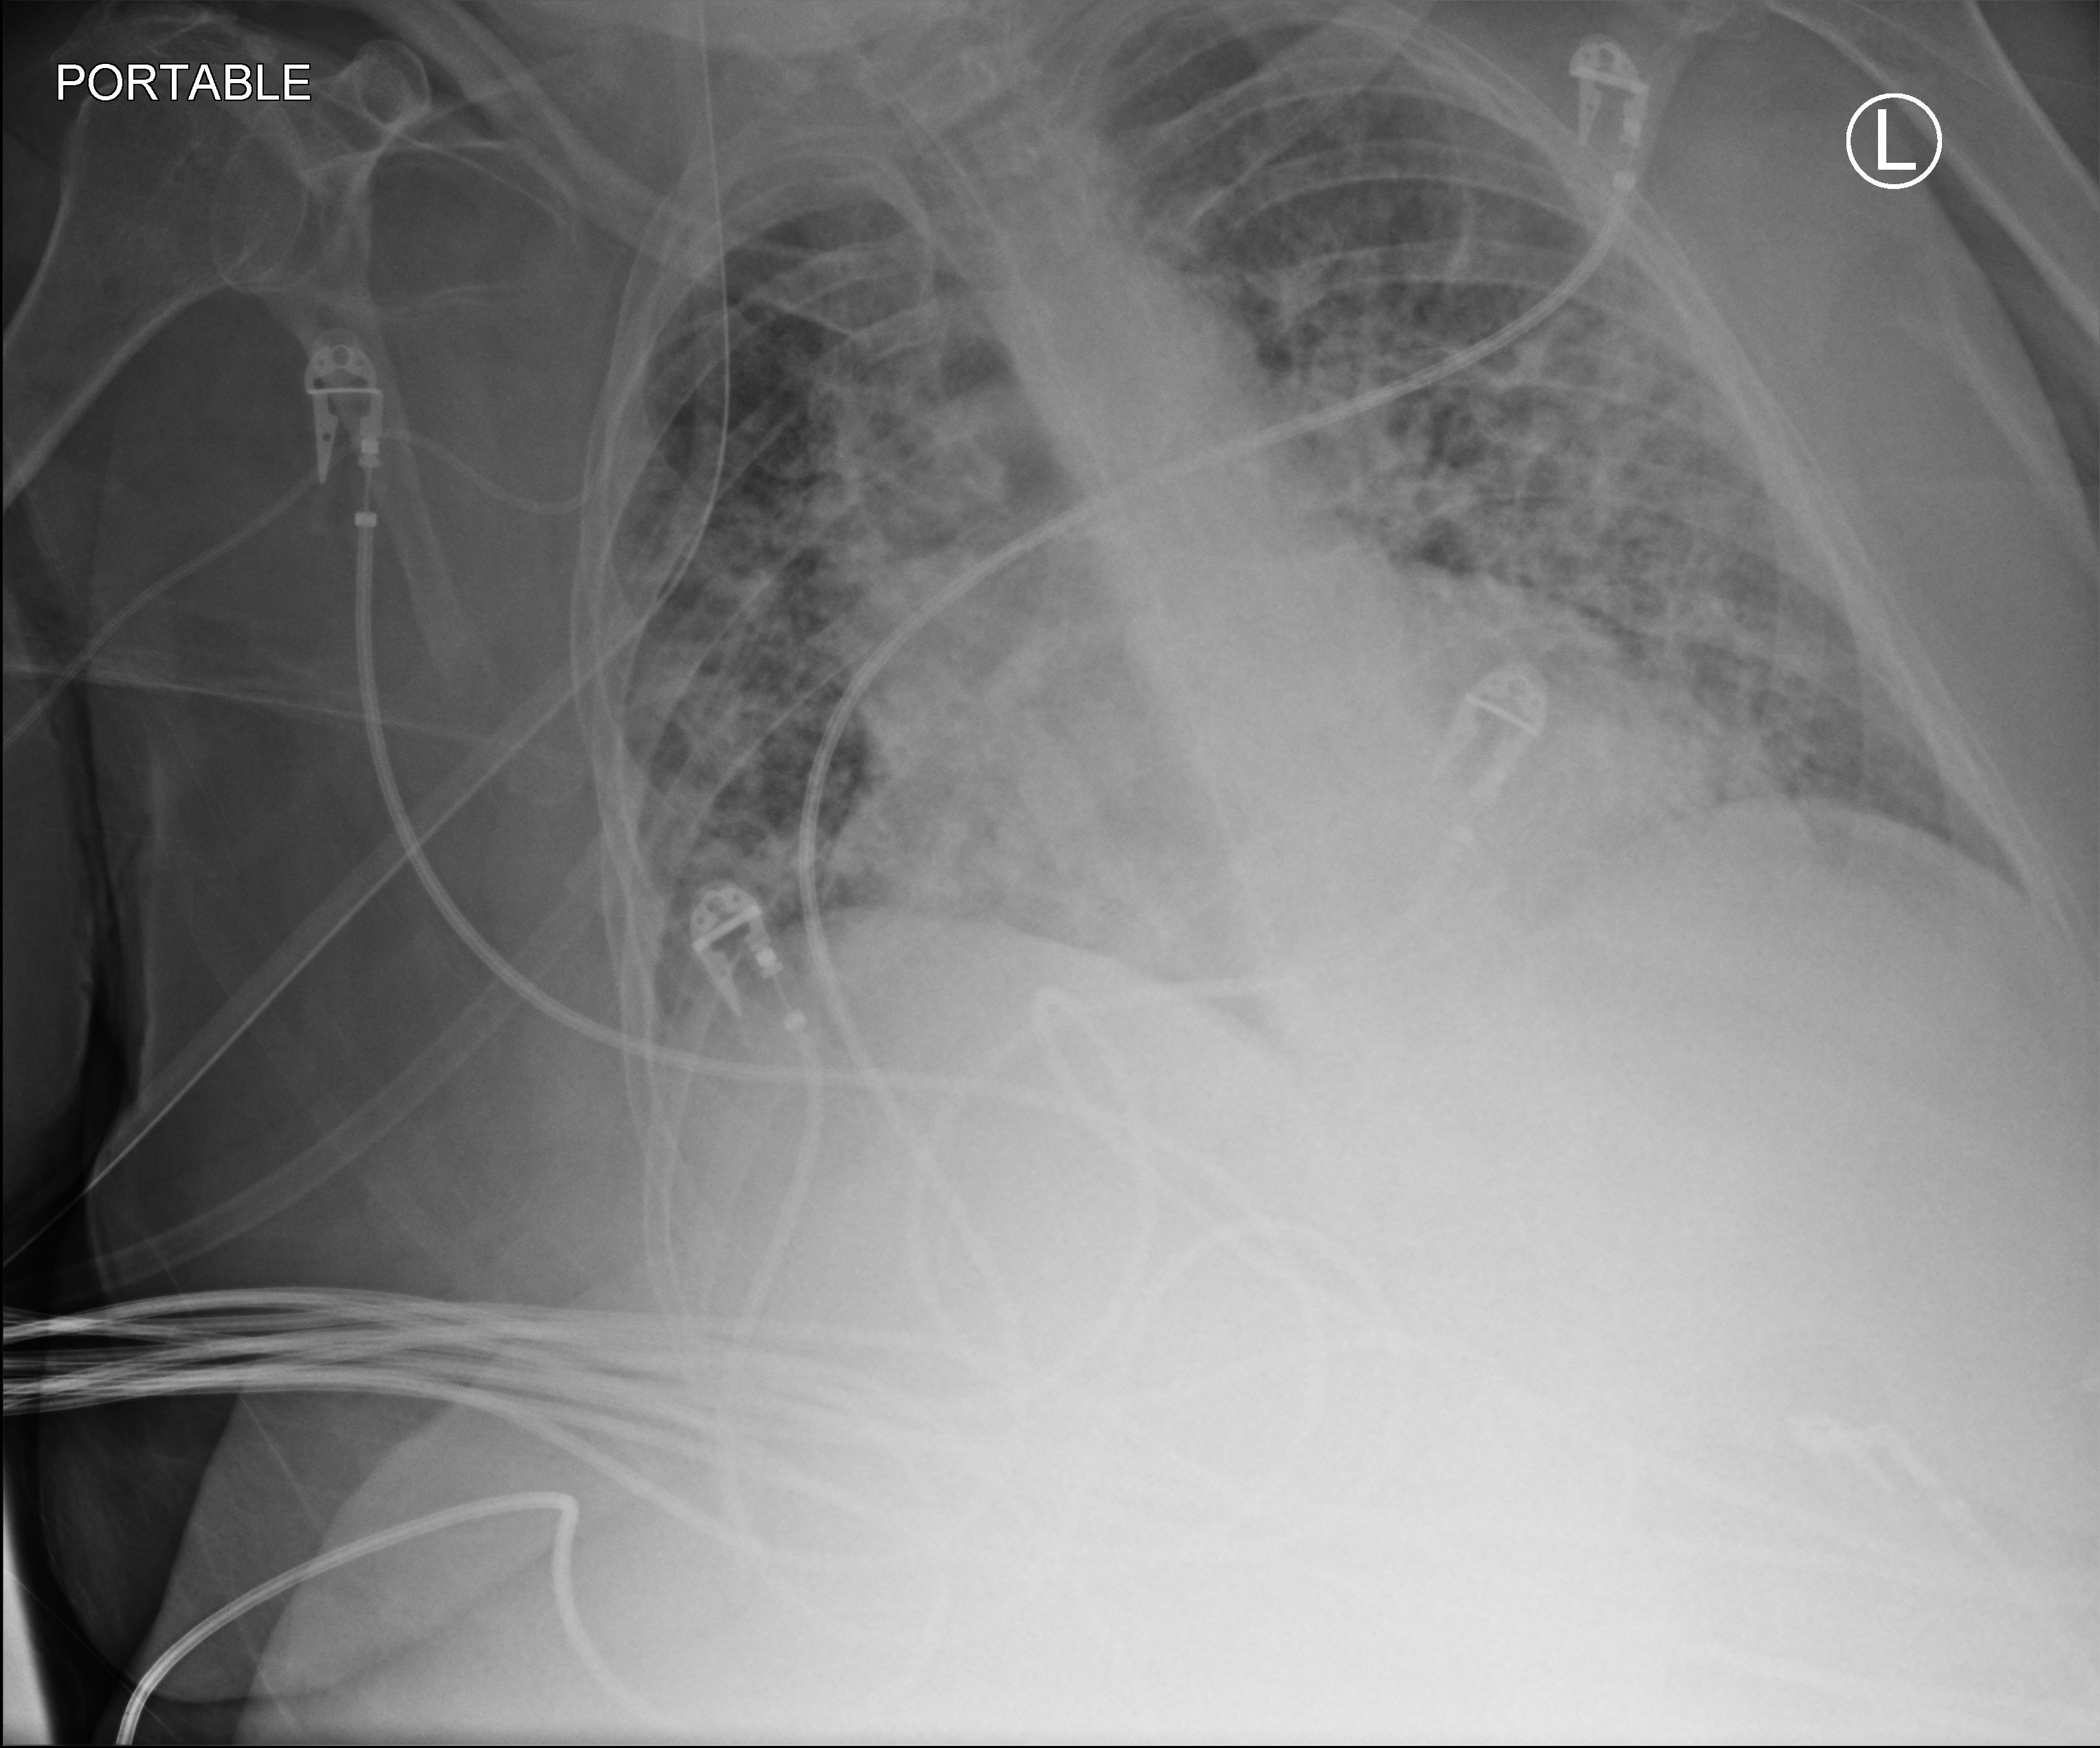
Bedside chest radiograph (computed radiography); anteroposterior (AP) projection. Patient hospitalised with COVID-19; female, aged 75–90 years.
From the hospital-stay record, not from the radiograph (when in the stay this image was taken is not recorded): length of hospital stay: 31 days; hypertension (admission record): yes.